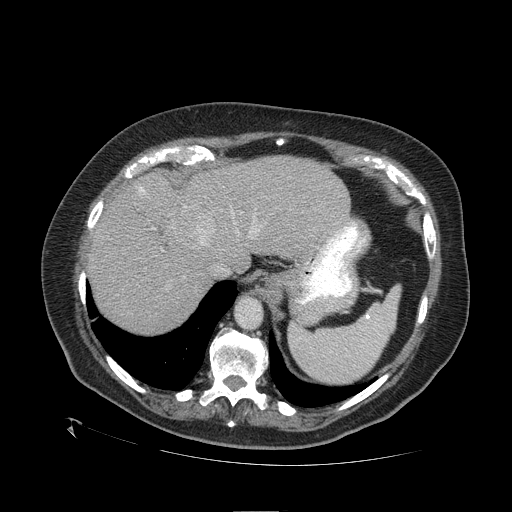
Contrast-enhanced abdominal CT (liver protocol), one axial slice; position 85 of 109 along the scan axis; reconstruction kernel STANDARD; one of 2 acquisitions stored at this slice position; soft-tissue window (W 400 / L 40 HU); 512 × 512 image matrix. From the clinical record (not read from this slice): diagnosis: hepatocellular carcinoma (patient treated with transarterial chemoembolisation; whether this scan precedes or follows treatment is not stated here); TNM stage (as recorded): Stage-I.
Annotated regions visible in this slice (semi-automatically segmented with operator editing):
- abdominal aorta: bounding box (x1, y1, x2, y2) in pixels: (236, 297, 261, 327)
- liver parenchyma outside the tumour (the mass and vessels are separate outlines, so this box may not span the whole liver): (88, 156, 352, 334)
- mass: (169, 204, 221, 250)
- liver vessels: (139, 187, 259, 233)